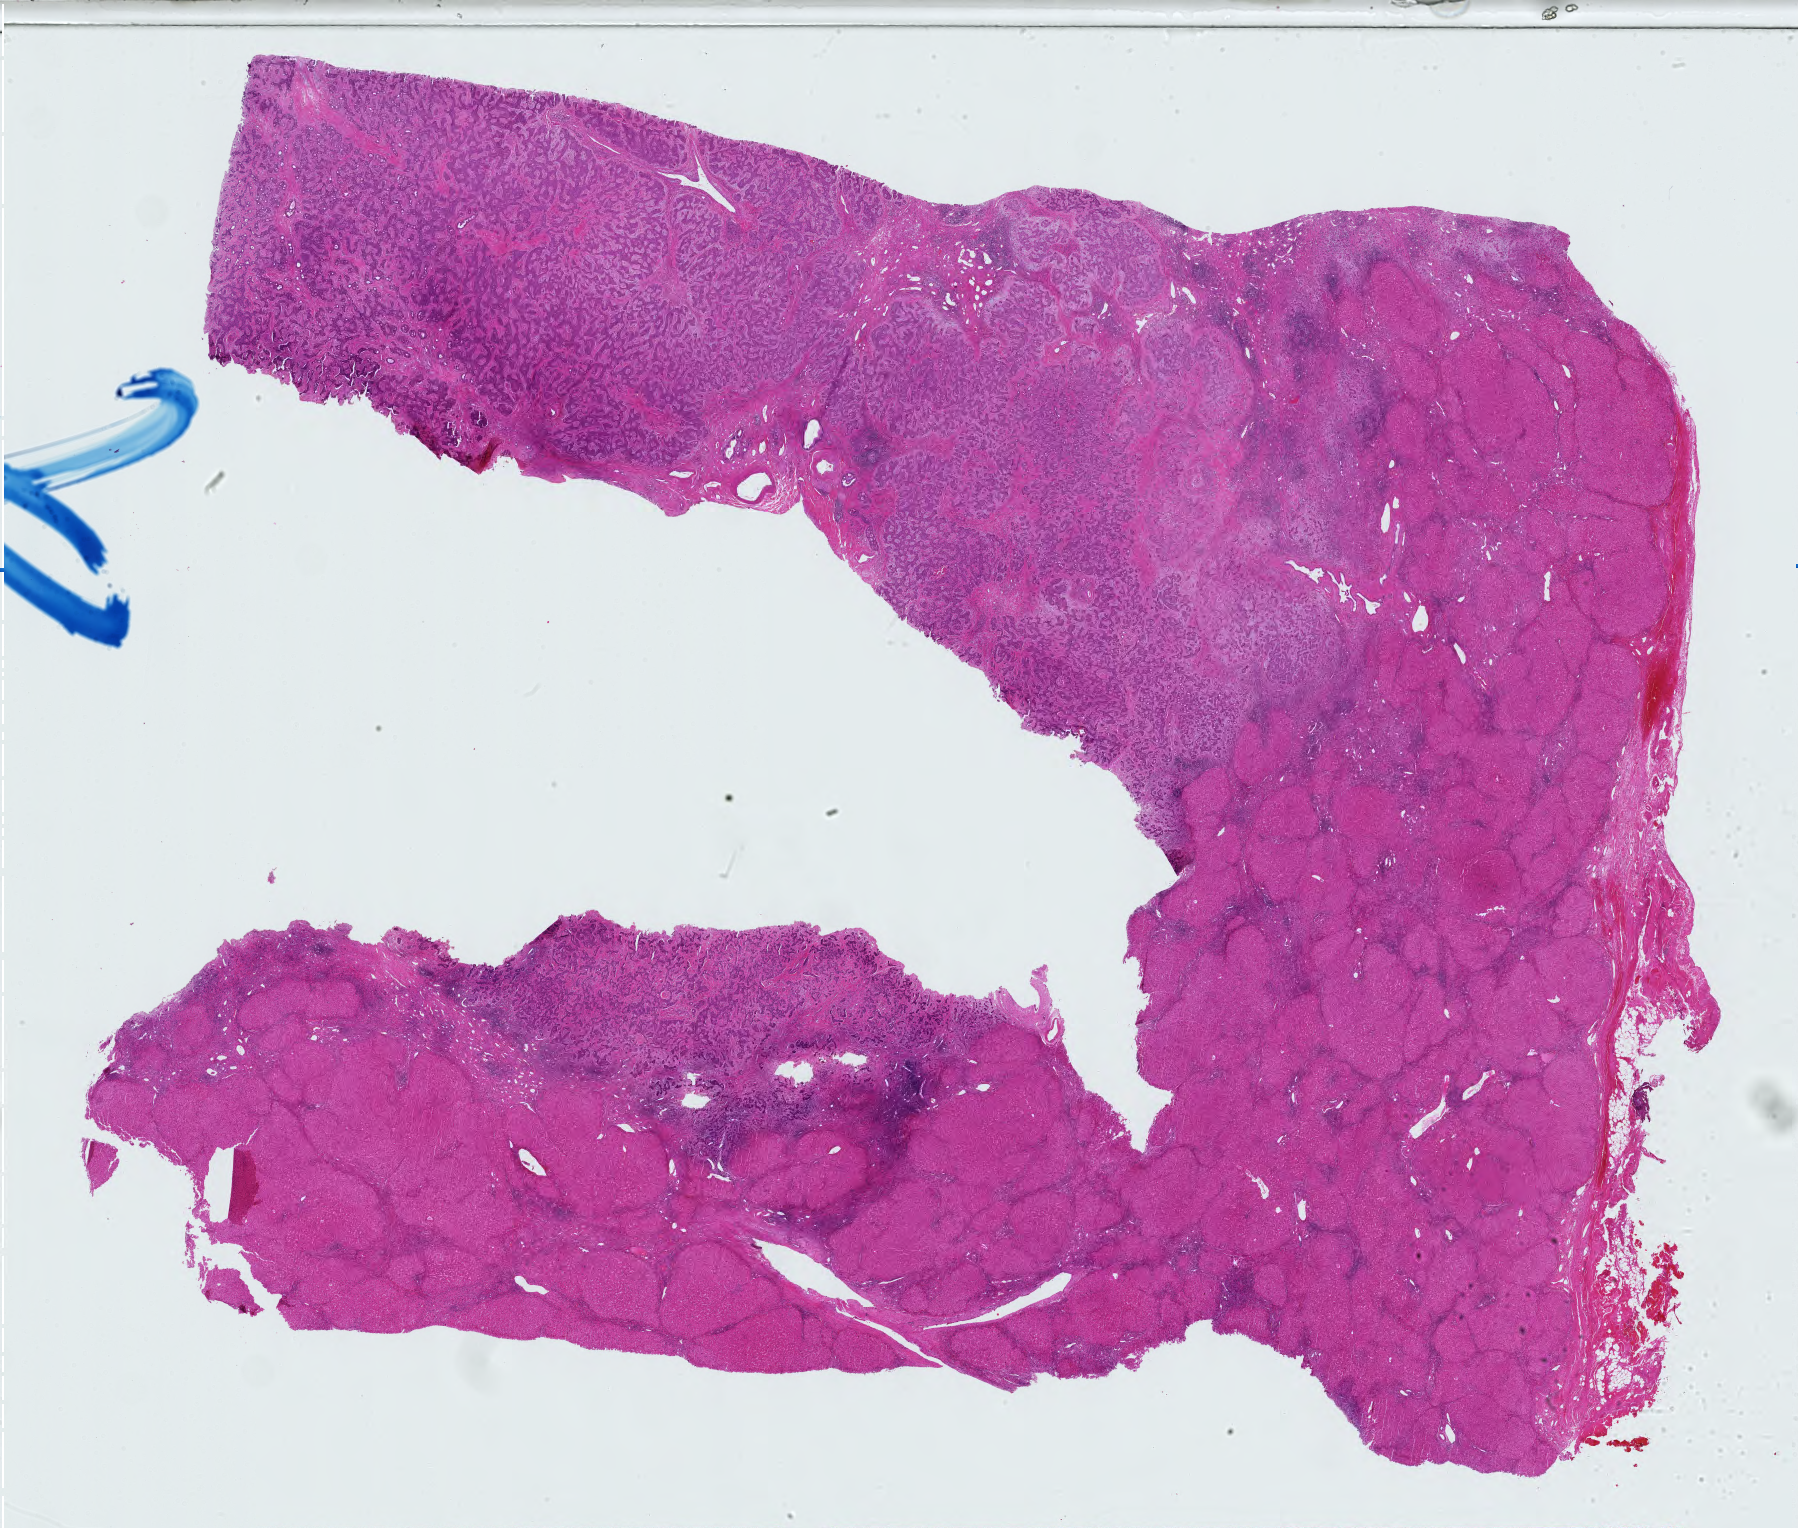
Digitized H&E tissue section (whole slide) — low-resolution overview of the scanned area, about 26.1 x 22.1 mm, FFPE section, sample: primary tumour, bile duct. Patient: female, age at initial diagnosis 71 years. Histologic grade: G2 (moderately differentiated).
- diagnosis: Cholangiocarcinoma (liver)
- AJCC pathologic stage: II (7th edition)
- TNM: T2b NX MX